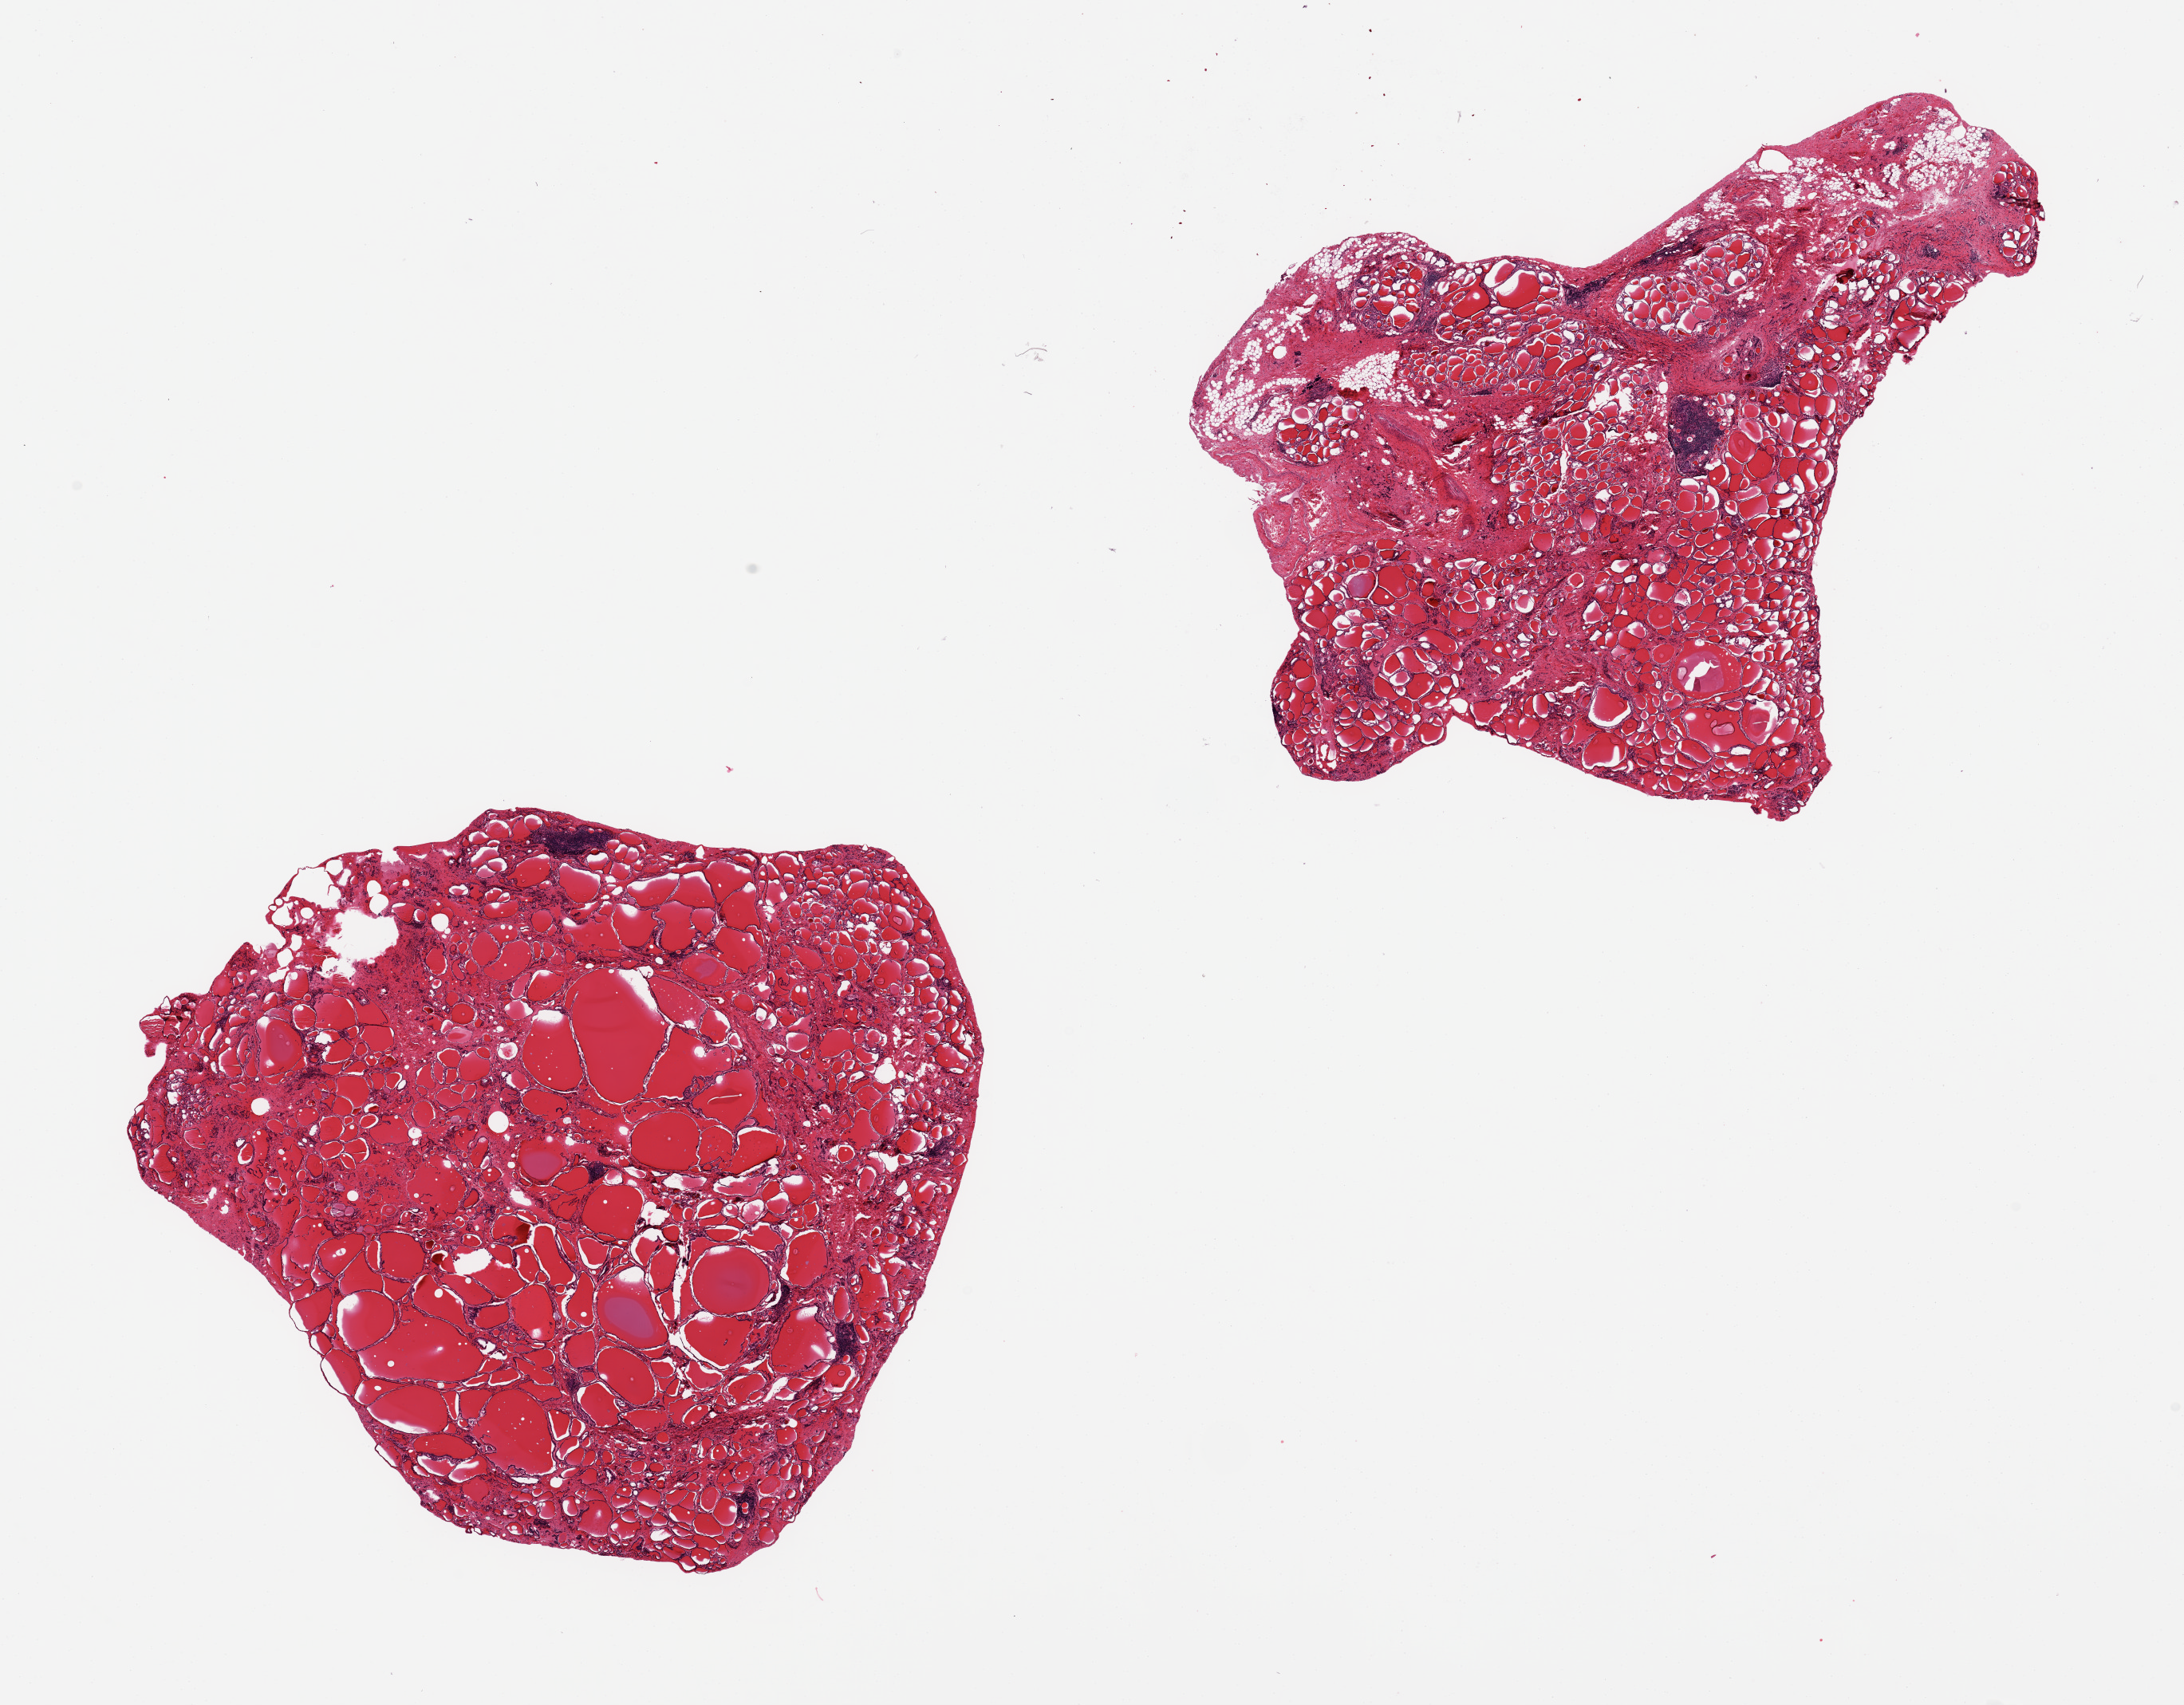
Haematoxylin and eosin whole-slide image, shown as a low-resolution overview of the whole scanned area (about 21.7 x 16.9 mm); PAXgene-fixed, paraffin-embedded tissue; section of thyroid (target tissue); tissue donor sample. Donor: female.
* reviewer comment on this tissue sample: 2 ~9x7 mm pieces